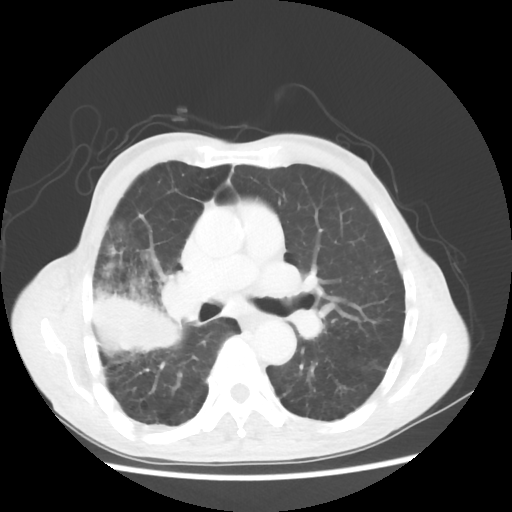
Chest CT, one axial slice. Position 30 of 58 along the scan axis. Reconstruction kernel STANDARD. 100 kVp. Lung window (W 1500 / L -600 HU). 5 mm slice thickness. 512 × 512 image matrix, field of view 351 × 351 mm. Male patient, age 75 years. From the clinical record (not read from this slice): clinical TNM (as recorded): T4 N1 M1.
Annotated regions visible in this slice (rectangle marked by the reading radiologist):
- lung tumour (recorded histology: adenocarcinoma): bounding box (x1, y1, x2, y2) in pixels: (87, 278, 194, 357)